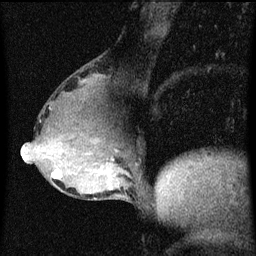
Breast MRI (dynamic contrast-enhanced), one sagittal slice; position 30 of 60 along the scan axis; dynamic contrast-enhanced series, image 2 of 3 at this slice position (ordered by acquisition); 1.5 T; TE 4.2 ms, TR 8 ms; 256 × 256 image matrix, field of view 180 × 180 mm. Female patient, age 49 years.
Structures marked on this image (semi-automatic segmentation, software-assisted and operator-edited):
- analysis volume of interest (the breast-tissue region the enhancement analysis was run in; not a lesion): box from (x=51, y=158) to (x=96, y=185) px
- tumour enhancement mask (voxels above the 70 % enhancement threshold inside the analysis volume of interest): (x=53, y=170)–(x=63, y=179)